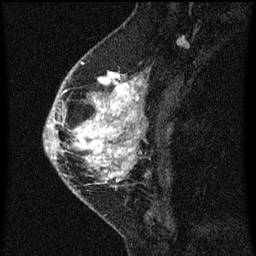
Breast MRI (dynamic contrast-enhanced), one sagittal slice. Position 25 of 60 along the scan axis. Dynamic contrast-enhanced series, image 2 of 3 at this slice position (ordered by acquisition). 1.5 T. TE 4.2 ms, TR 8 ms. 2 mm slice thickness. 256 × 256 image matrix, field of view 180 × 180 mm. Patient: female, 46 years.
Annotated regions visible in this slice (semi-automatic segmentation, software-assisted and operator-edited):
- analysis volume of interest (the breast-tissue region the enhancement analysis was run in; not a lesion): bounding box [x1, y1, x2, y2] px = [48, 68, 145, 195]
- tumour enhancement mask (voxels above the 70 % enhancement threshold inside the analysis volume of interest): [48, 70, 145, 189]